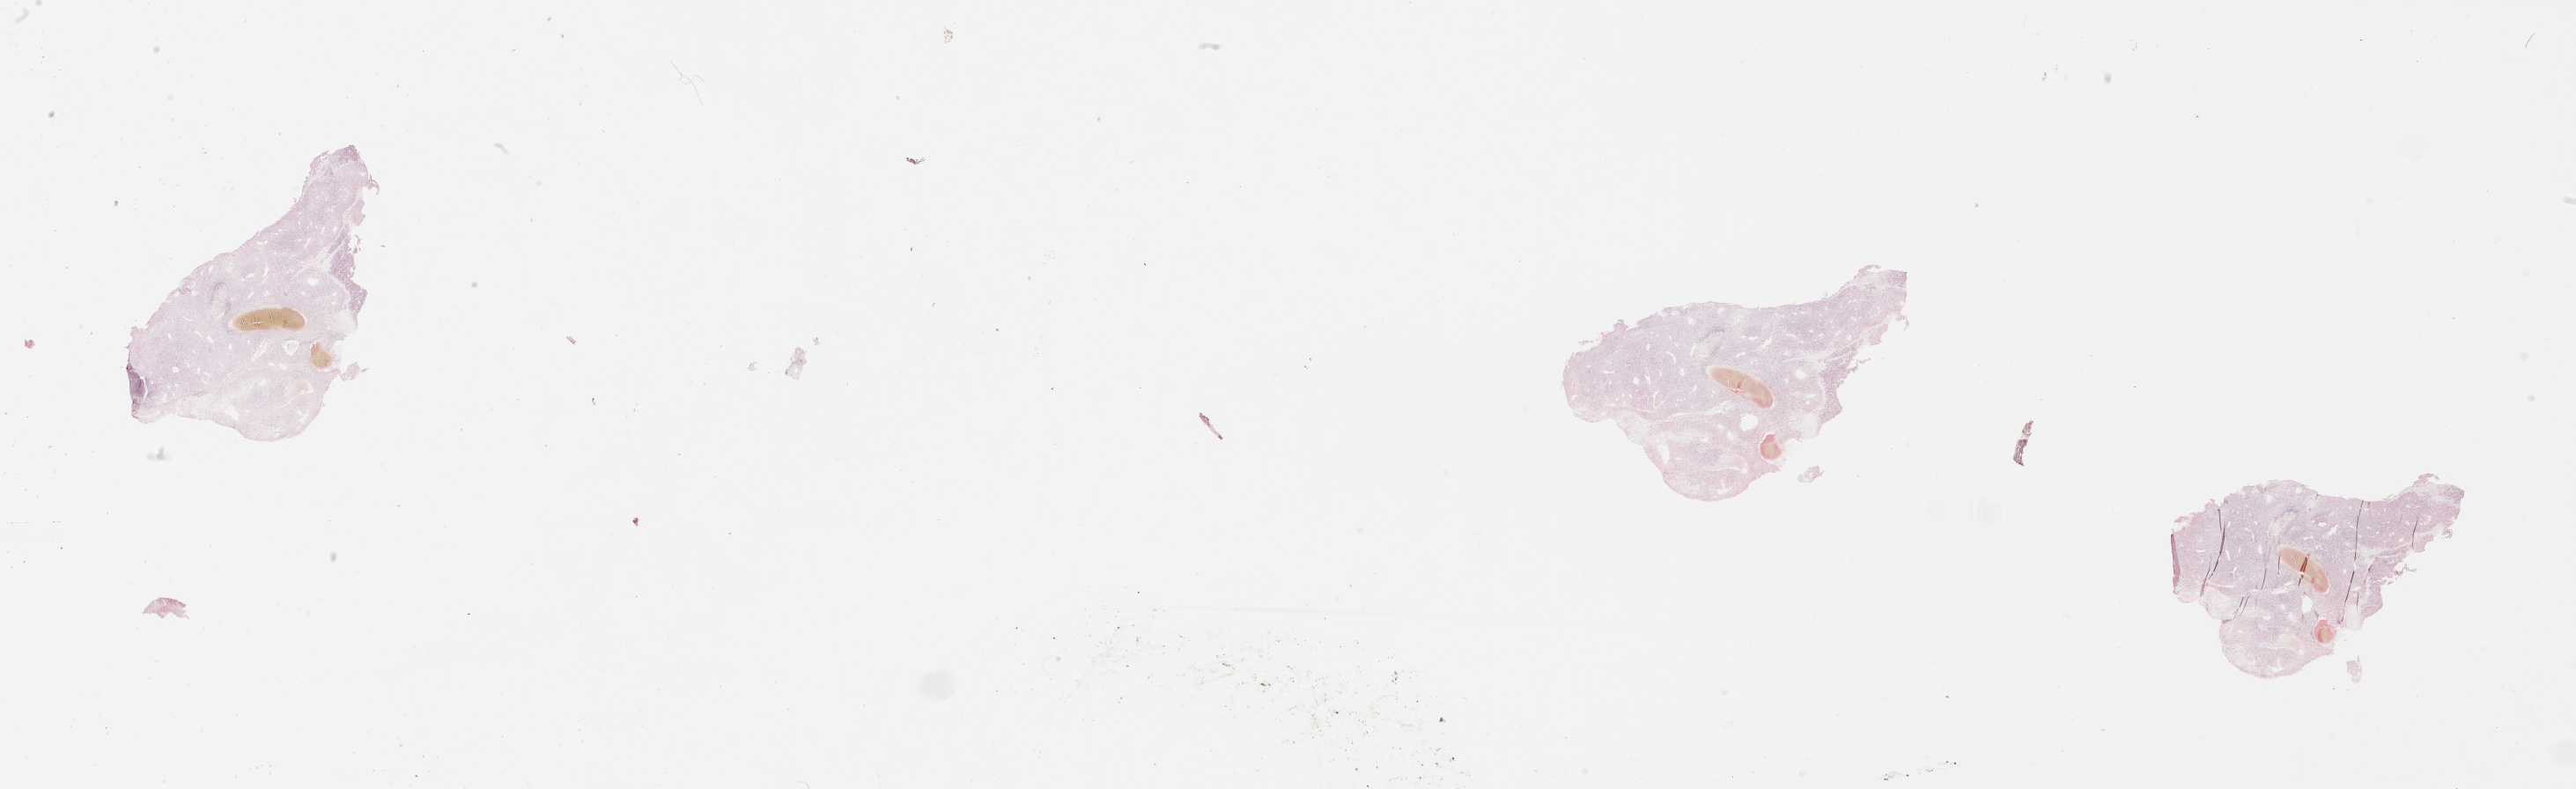
Digitized H&E tissue section (whole slide), low-resolution overview of the scanned area, about 46.3 x 14.2 mm. Tumour tissue sample. Patient: male, age 60 years.
* patient diagnosis (cohort enrolment): sarcoma (site not recorded at cohort level)
* primary tumour site (as recorded): lower extremity